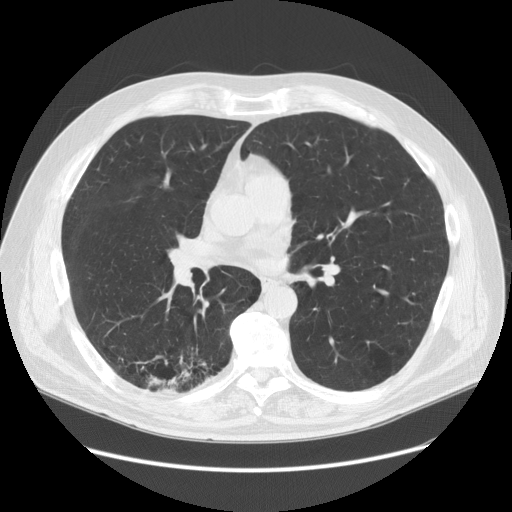
Low-dose screening chest CT, axial slice. First (baseline) screen. Lung window (W 1500 / L -600 HU). 2.5 mm slice thickness. Standard (soft-tissue) reconstruction kernel (STANDARD). 512 × 512 image matrix. Male, age 68 years at enrolment. Former smoker at enrolment.
• Lesion marked by an expert reader, bounding box [x1, y1, x2, y2] px = [128, 342, 225, 414].
• Screening reader's record for this exam (one nodule recorded; not confirmed to be the boxed lesion): non-calcified nodule or mass ≥4 mm, right lower lobe, 37 × 20 mm, spiculated (stellate) margins, soft tissue attenuation.
• Official screen result: positive, change unspecified: nodule(s) >= 4 mm or enlarging nodule(s), mass(es), or other non-specific abnormalities suspicious for lung cancer.
• Participant outcome: lung cancer diagnosed 24 days after this screen — adenosquamous carcinoma, right lower lobe, poorly differentiated (G3), stage IIIA (AJCC 6th edition), 30 mm at pathology.